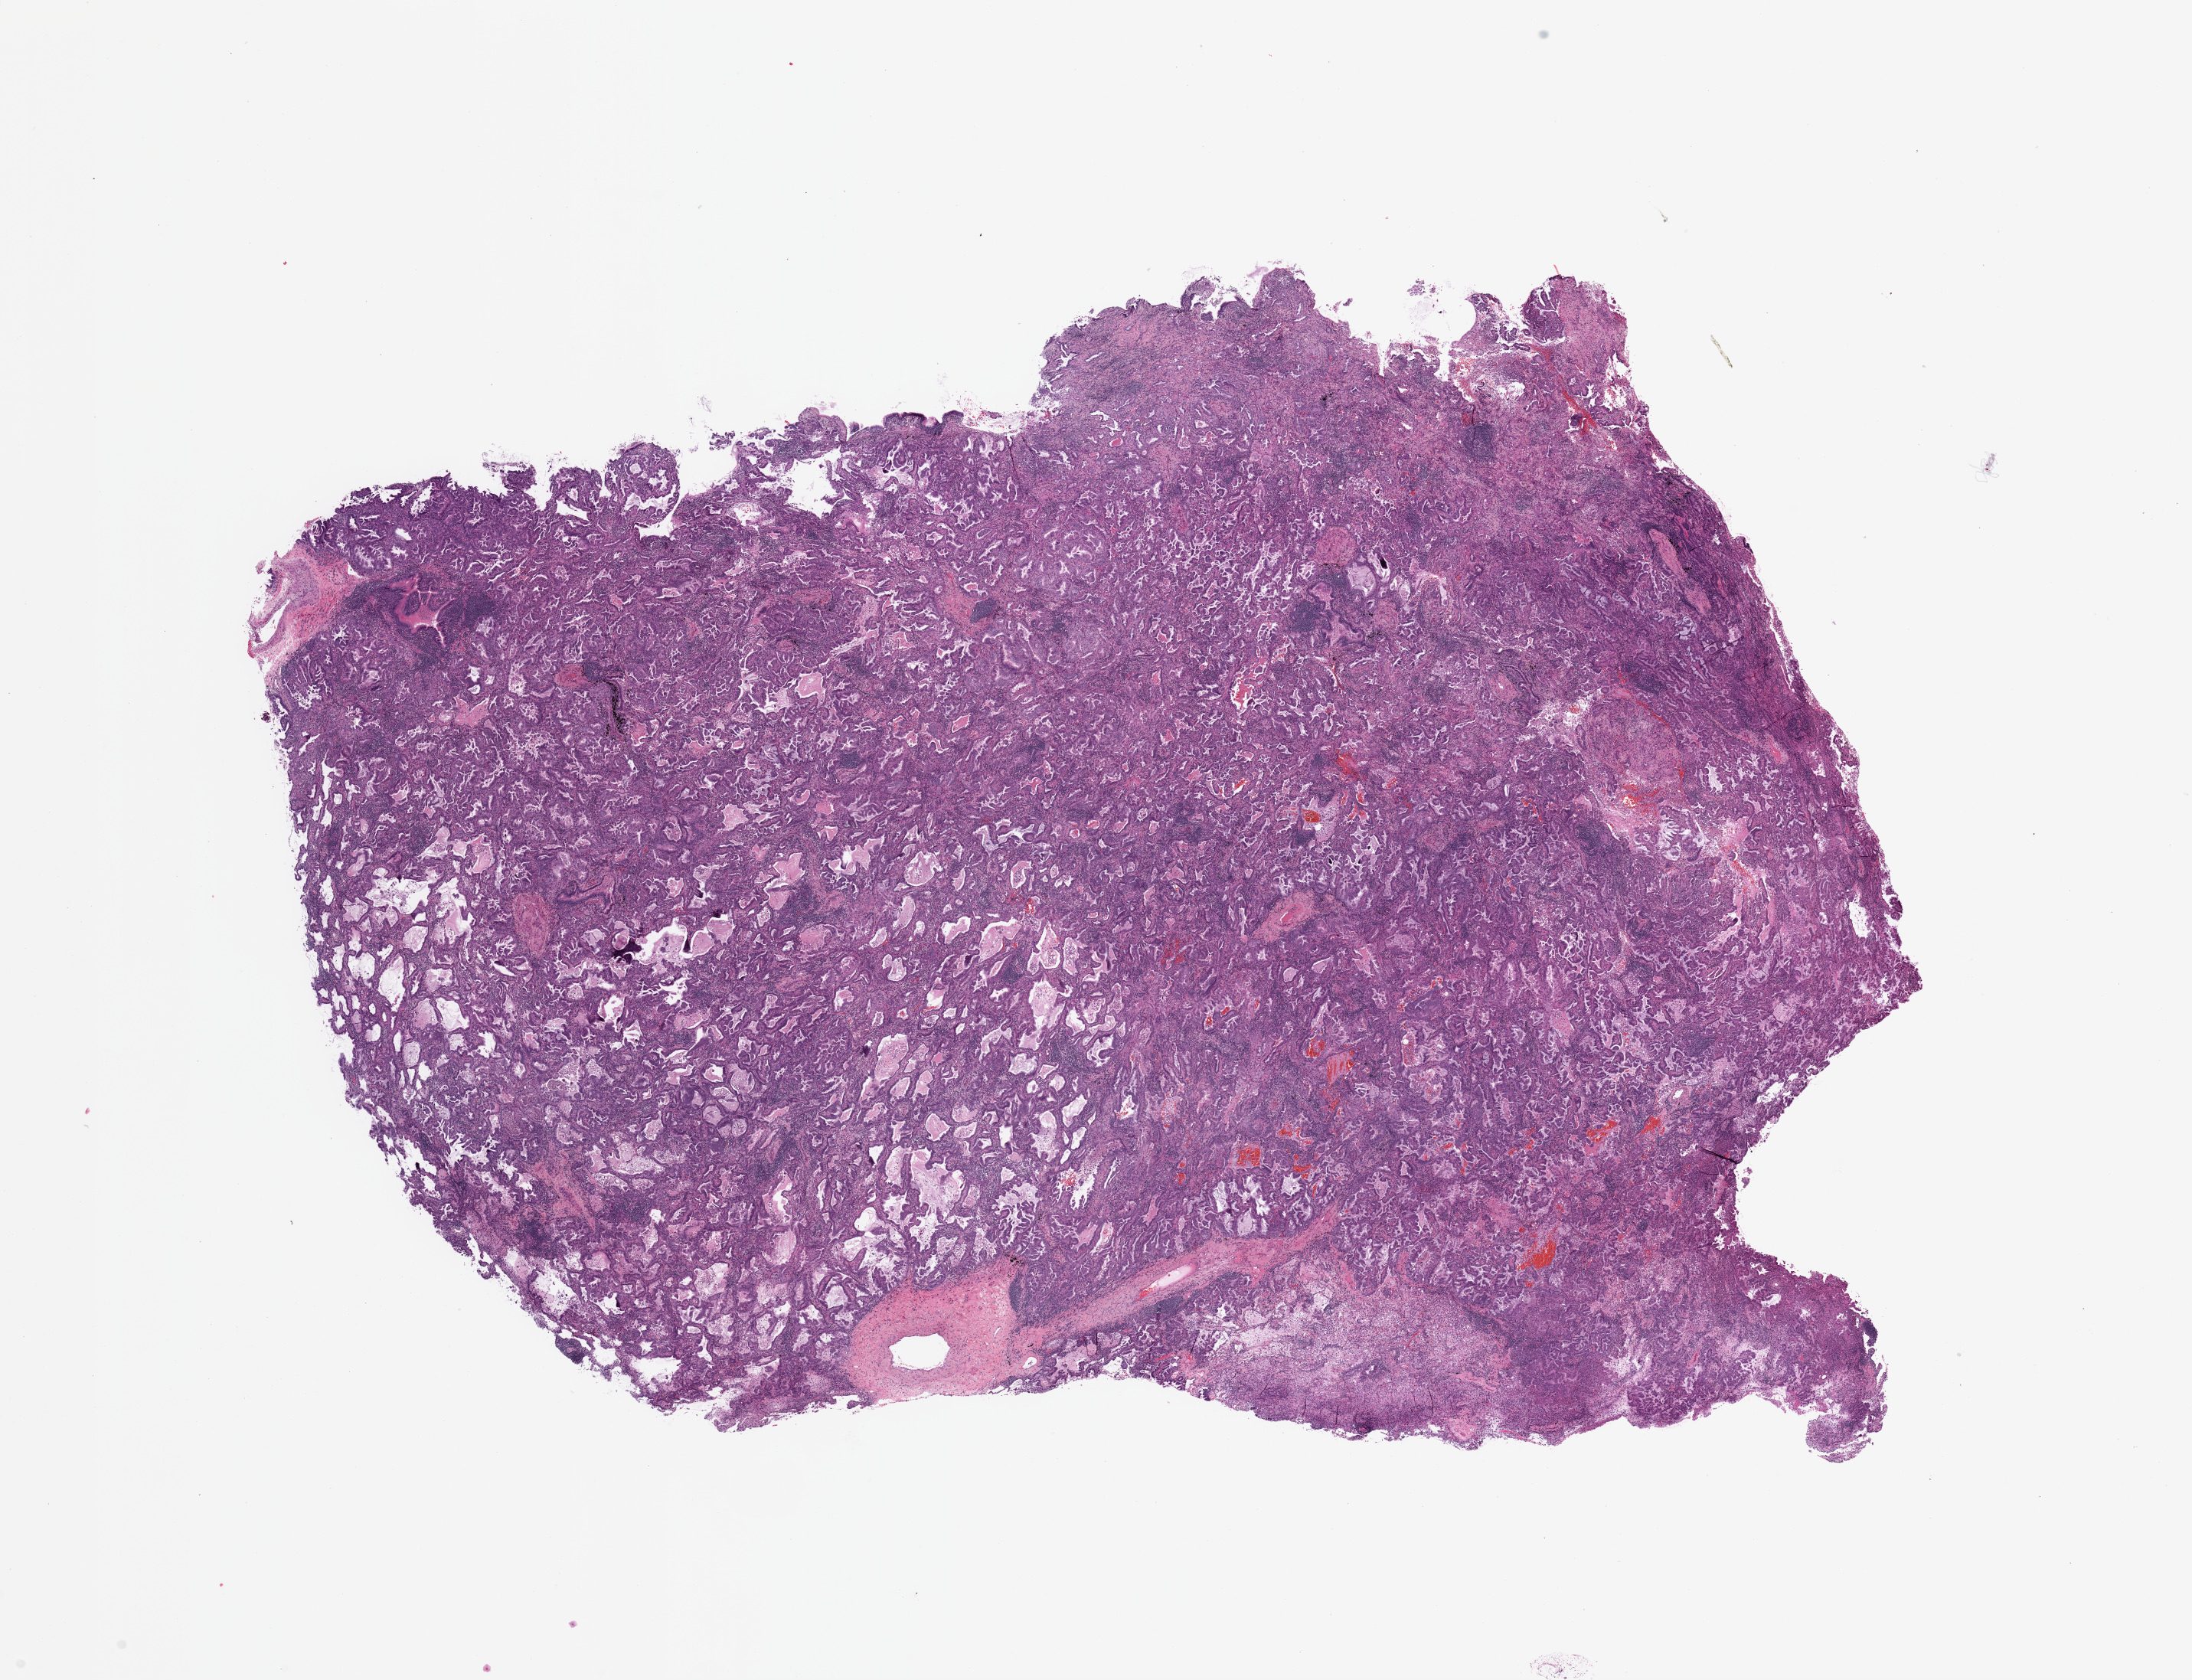
H&E whole-slide image, a low-resolution overview of the entire scanned area, about 22.6 x 17.4 mm (from a 20x scan). Tumour tissue sample, lung. Male, 76 y/o. Histologic grade: G2 (moderately differentiated).
- AJCC pathologic stage: IB
- diagnosis: Adenocarcinoma, NOS
- primary tumour site (as recorded): right lower lobe